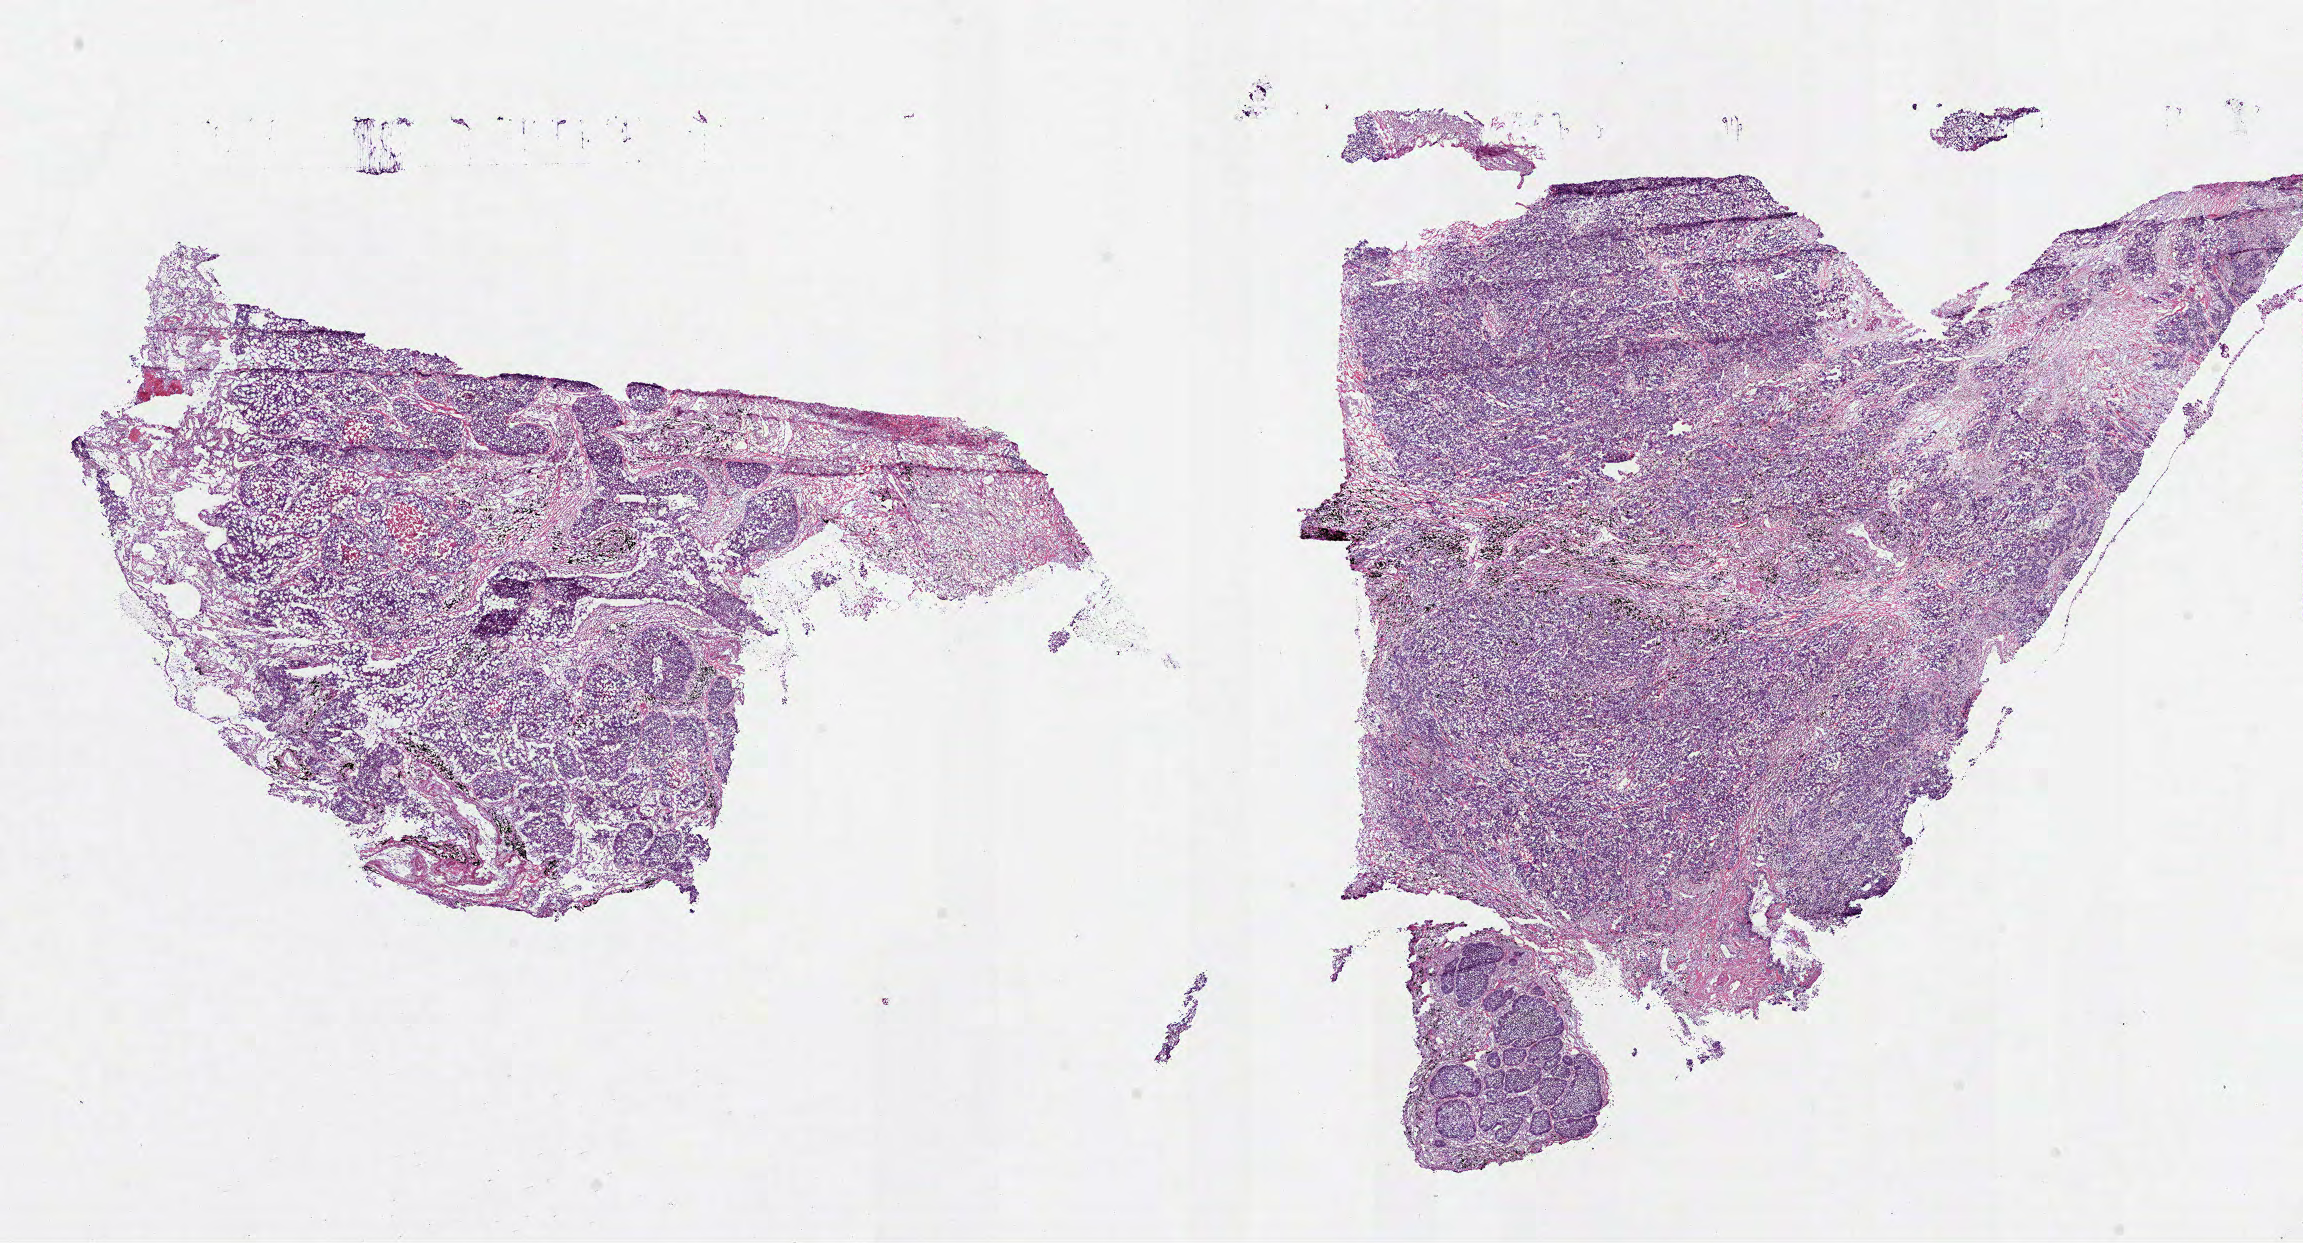
H&E whole-slide image — shown as a low-resolution overview of the whole scanned area (about 18.6 x 10.0 mm, from a 40x scan), frozen section from the top of the tissue portion, lung, primary tumour sample. Female, age 75 years at initial diagnosis. Slide review estimates, as recorded: tumour cells 90%, tumour nuclei 80%, normal cells 0%, stromal cells 5%, necrosis 5%. Infiltration values recorded for this section: lymphocyte infiltration 10%, monocyte infiltration 2%, neutrophil infiltration 5%.
Histologic diagnosis: Adenocarcinoma, NOS (upper lobe, lung). AJCC pathologic stage: IB.